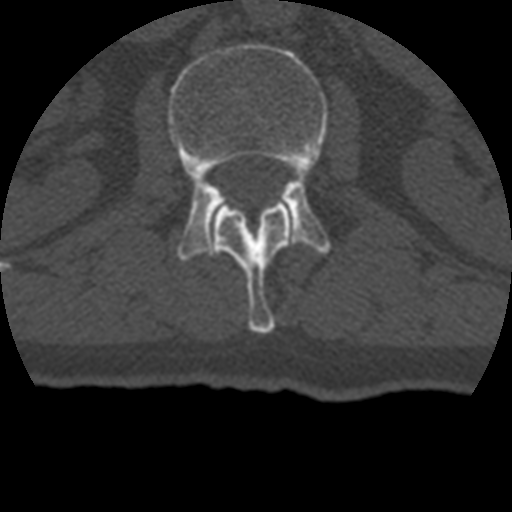
CT including the spine, one axial slice. Position 130 of 399 along the scan axis. Reconstruction kernel STANDARD. 120 kVp. Bone window (W 1800 / L 400 HU). 1.25 mm slice thickness. 512 × 512 image matrix. Patient age 69 years. Case-level facts recorded for this patient, not image findings: primary cancer: prostate.
Annotated regions visible in this slice (semi-automatically segmented with operator editing):
- L1 vertebra: box from (x=211, y=200) to (x=294, y=334) px
- L2 vertebra: (x=168, y=43)–(x=331, y=261)